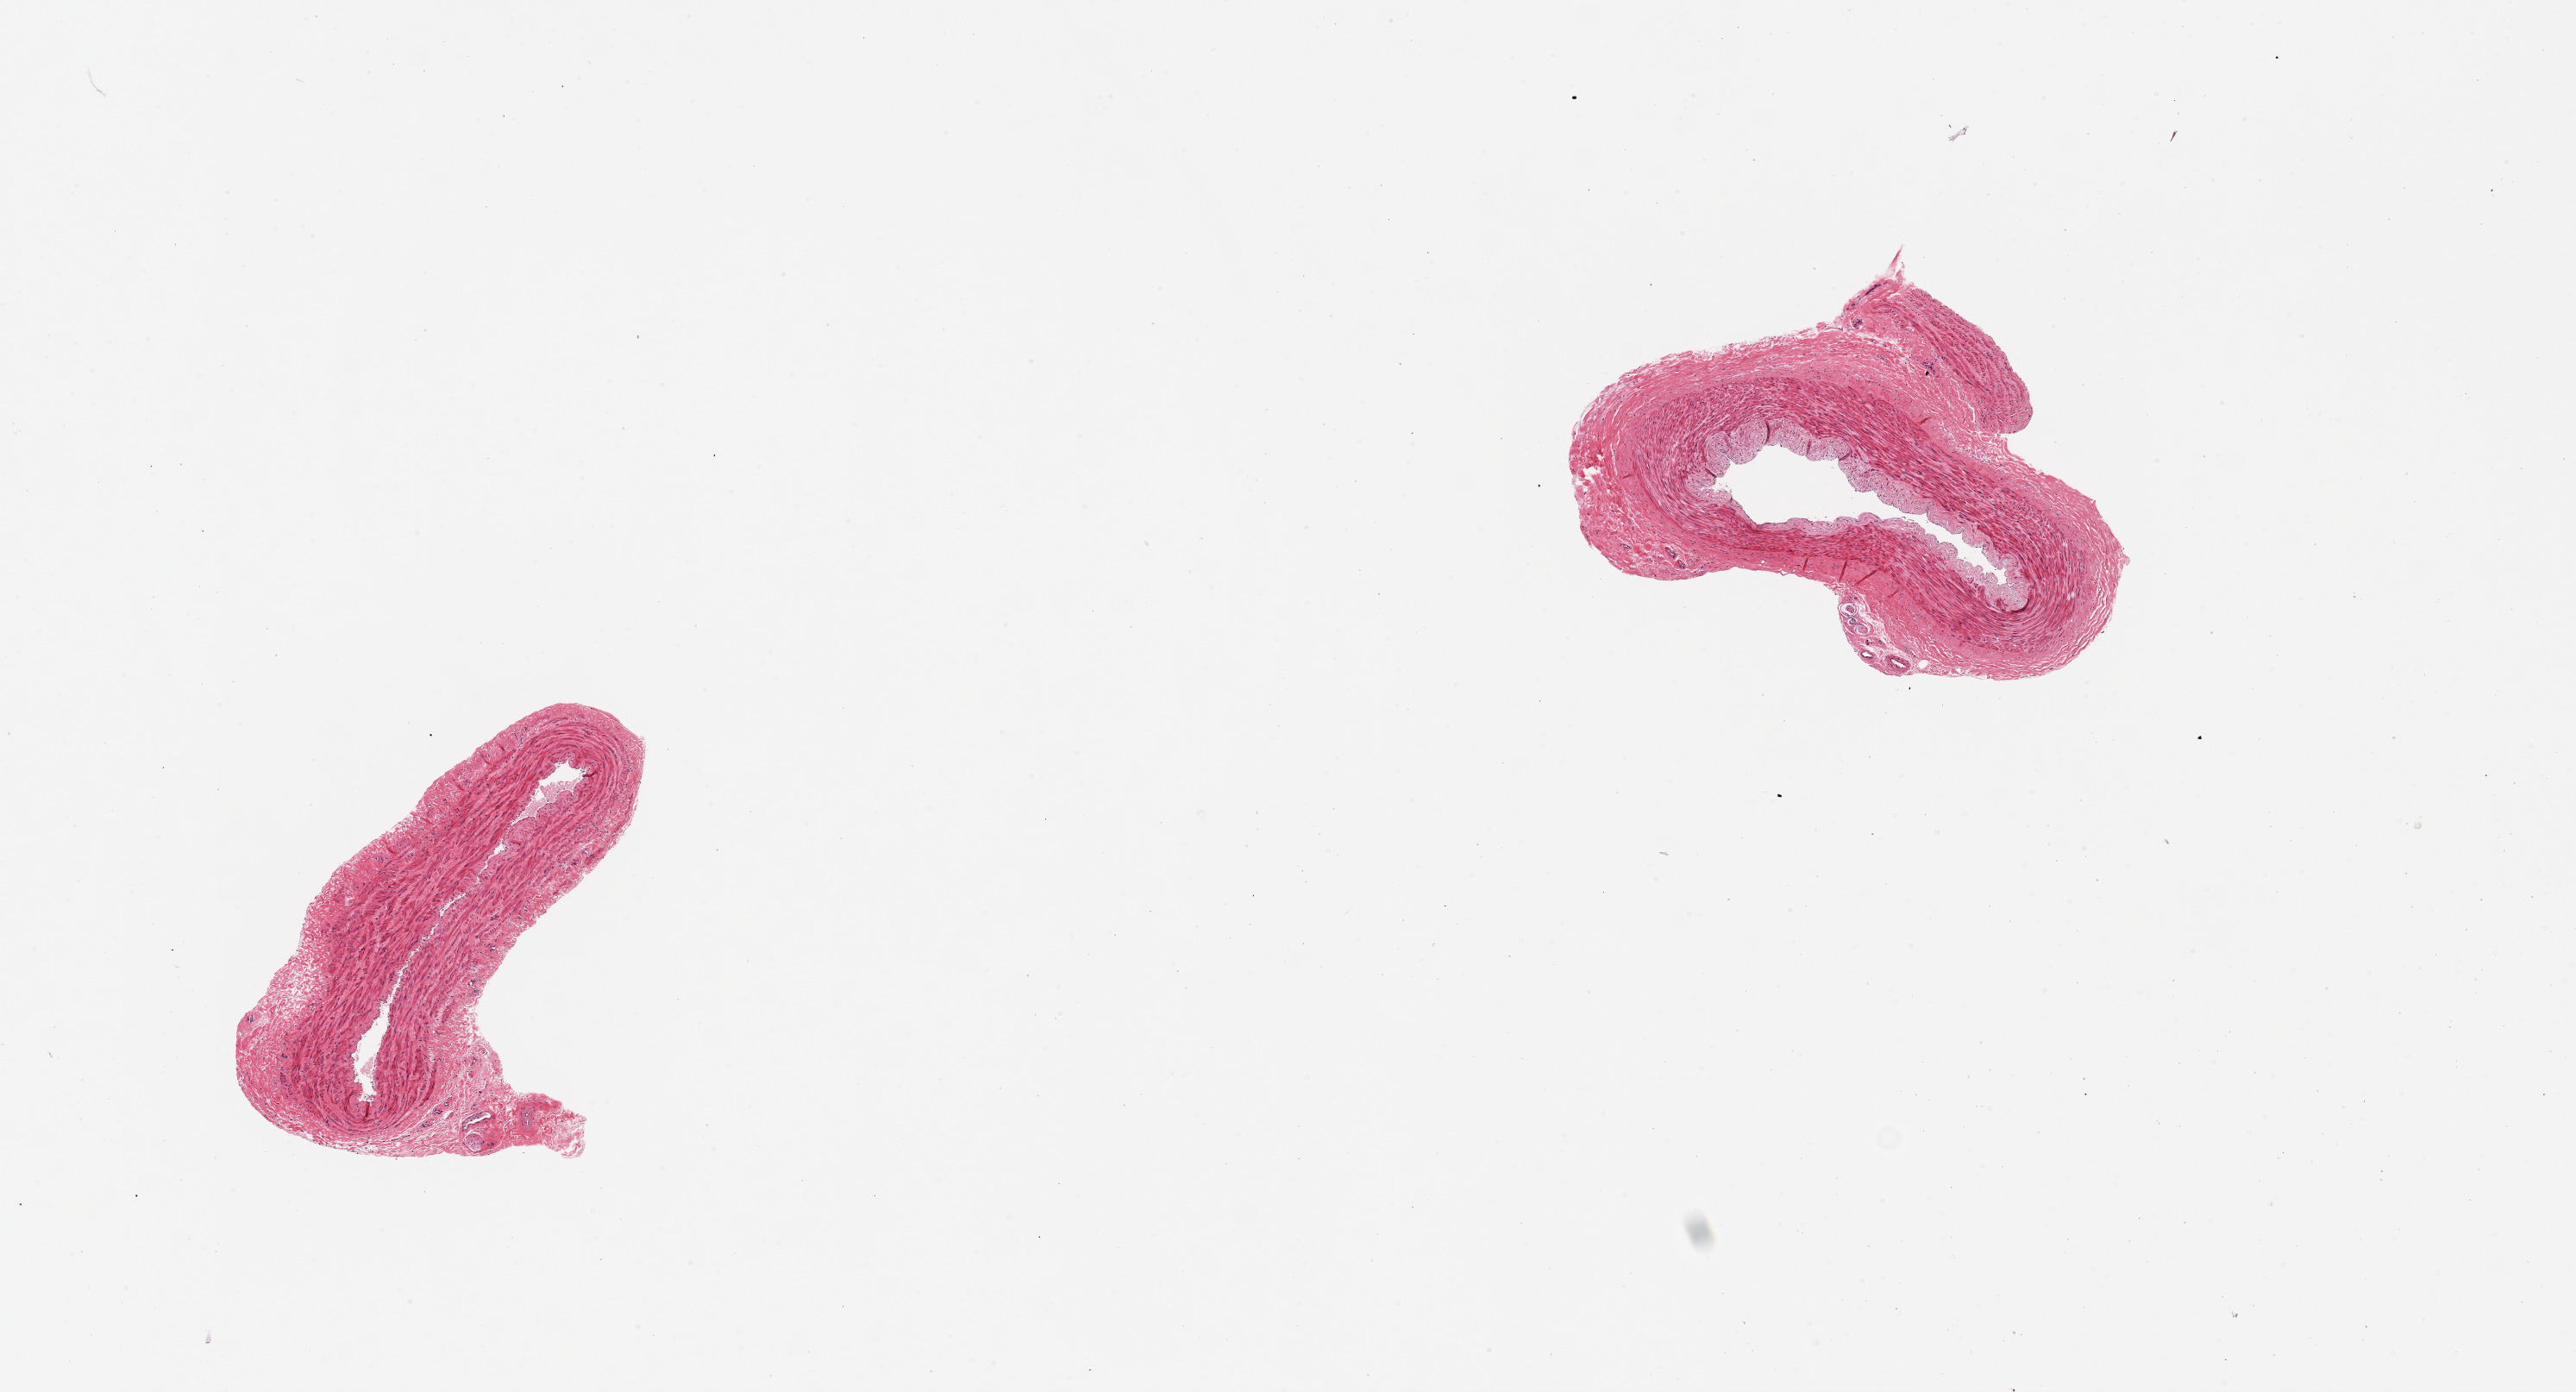
Whole-slide image, H&E stain — whole scanned area (about 11.8 x 6.4 mm, slide scanned at 20x) shown as a low-resolution overview. PAXgene-fixed, paraffin-embedded tissue. Section of tibial artery (target tissue). Tissue donor sample. Donor: male.
Pathologist's review note for this sample: 2 pieces, well-trimmed of fat.